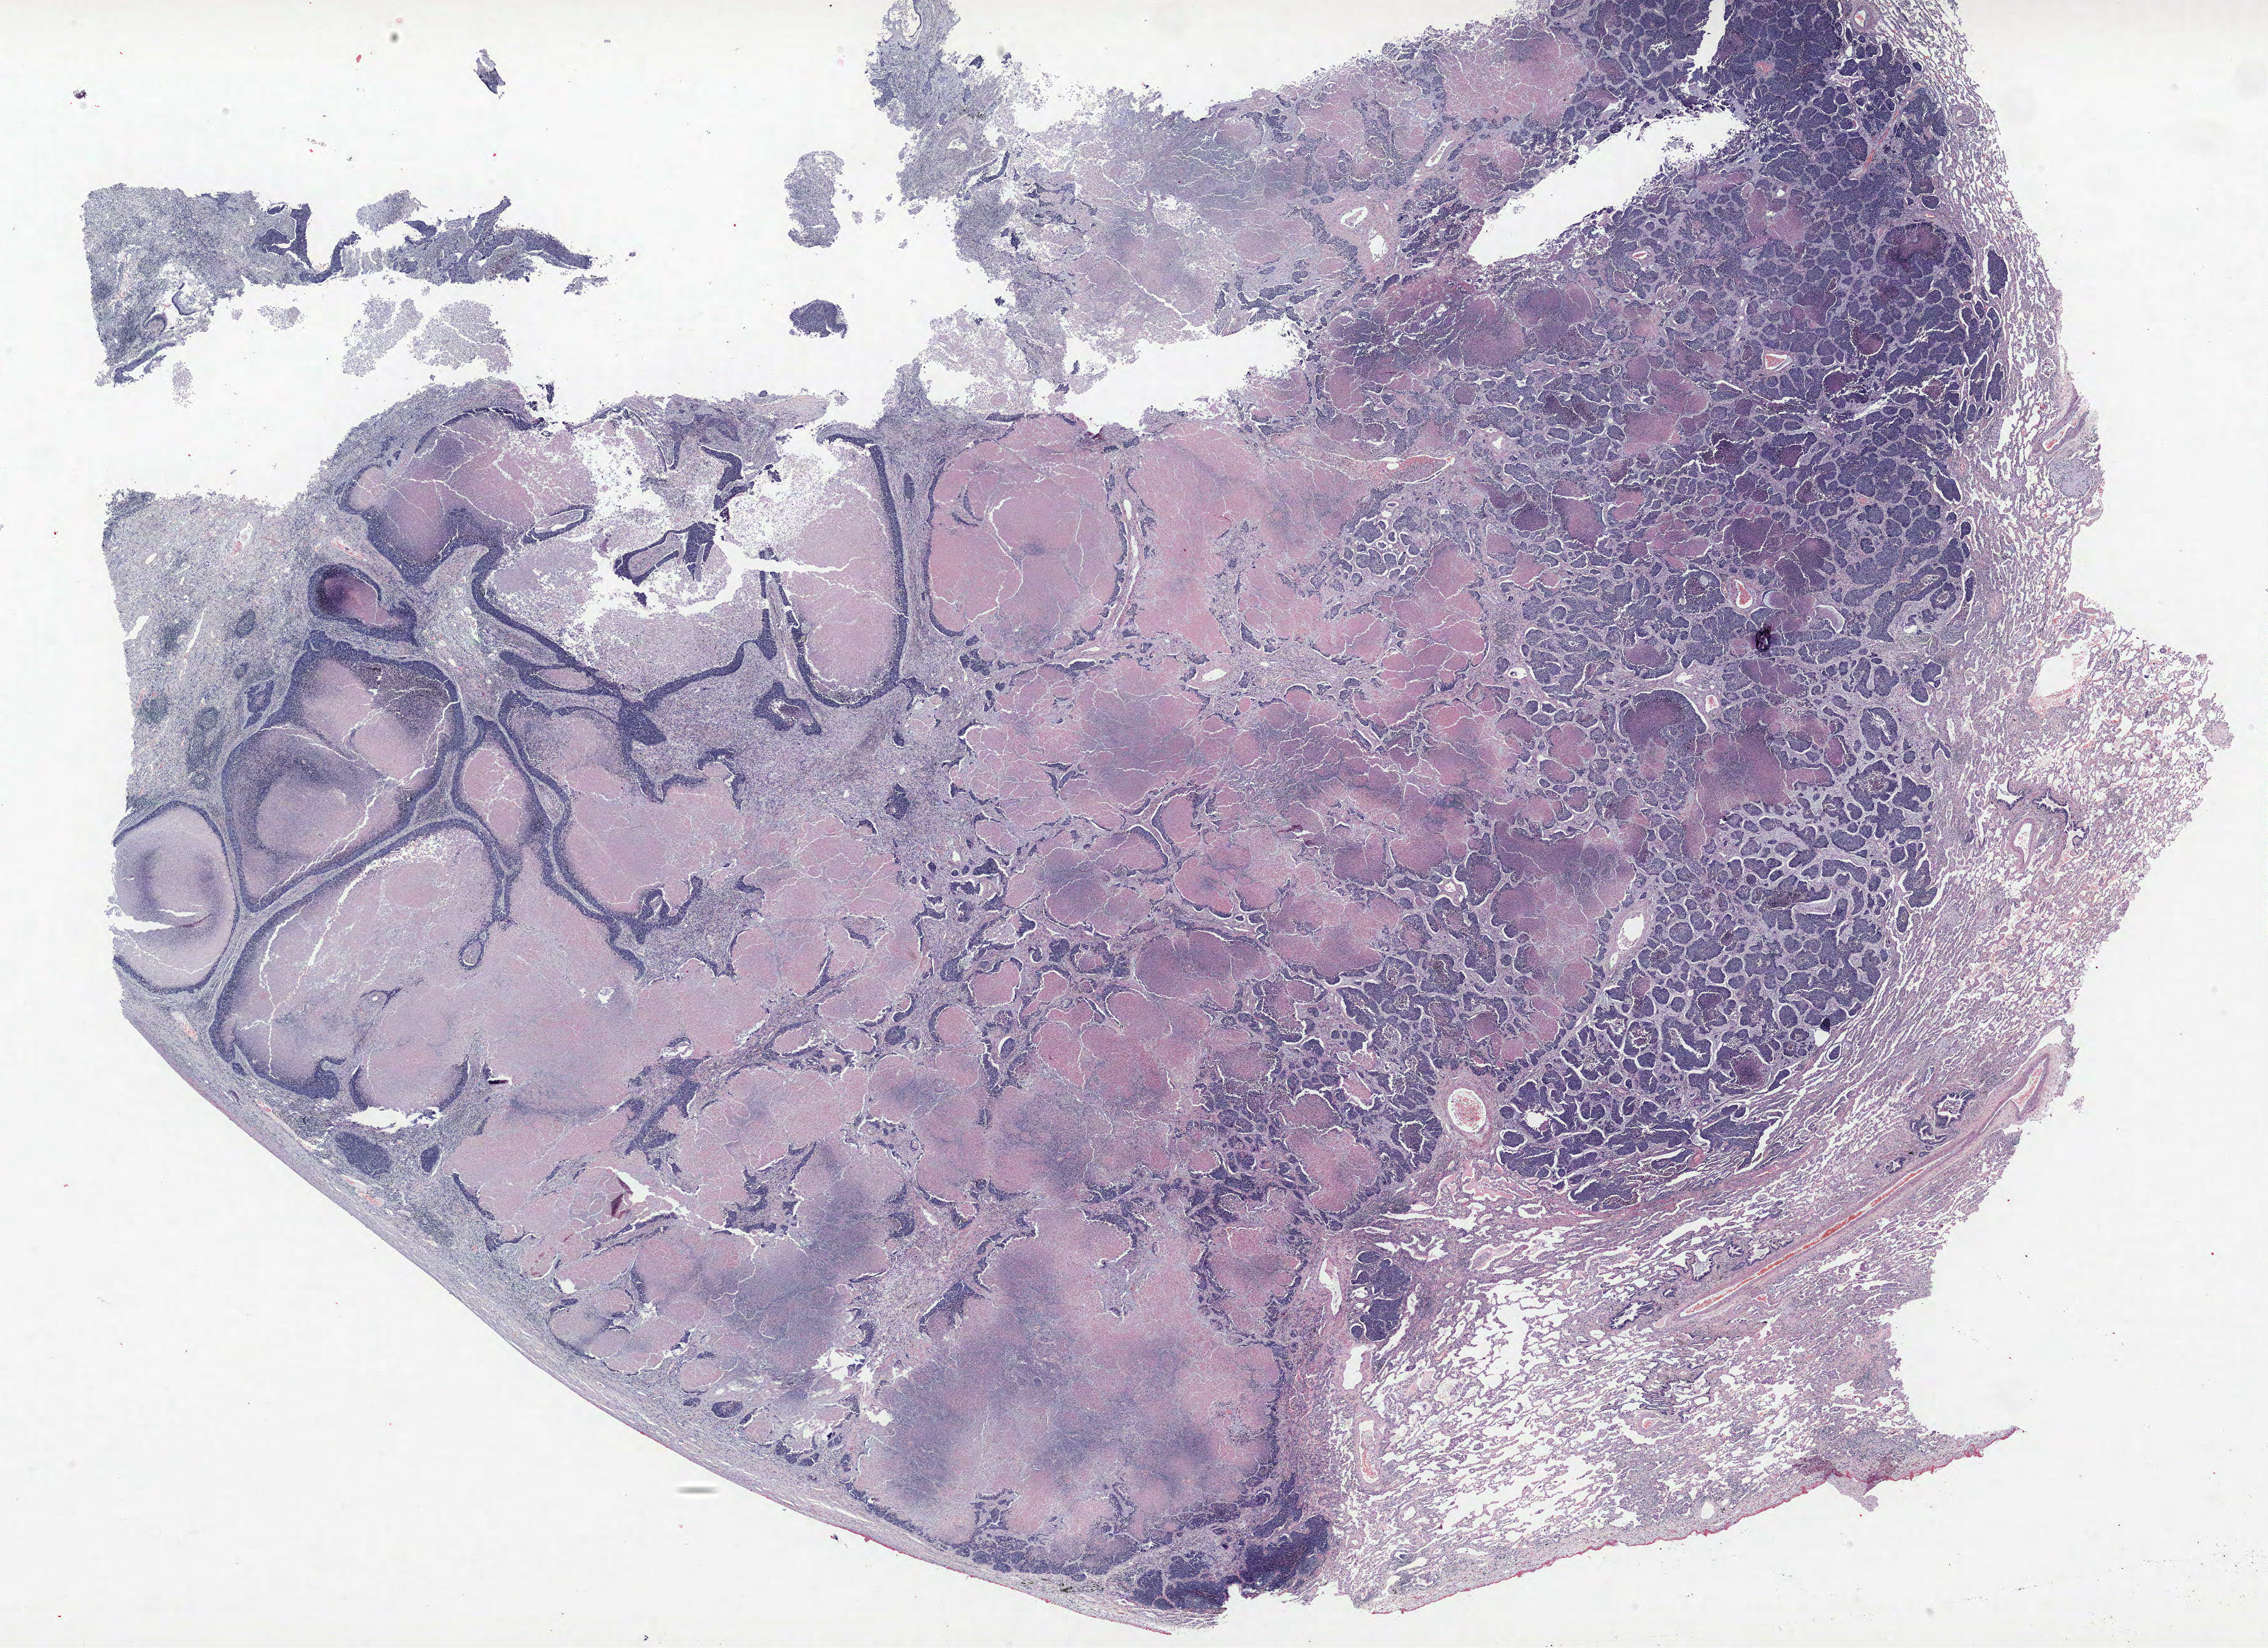
Whole-slide histology image, H&E — low-resolution overview of the scanned area, about 28.8 x 20.9 mm; FFPE section; lung. Male, age 68 at enrolment. Grade: moderately differentiated (G2).
• primary tumour location (clinical record): right lower lobe
• participant's lung-cancer diagnosis: Adenosquamous carcinoma
• stage (AJCC 6th edition): IB
• tumour size (pathology): 40 mm